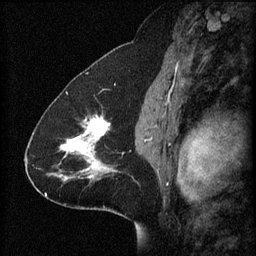
Breast MRI (dynamic contrast-enhanced), one sagittal slice; position 39 of 60 along the scan axis; 3 images stored at this slice position (order not interpretable as contrast timing); 1.5 T; TE 4.2 ms, TR 8.2 ms; 2 mm slice thickness; 256 × 256 image matrix, field of view 200 × 200 mm. Patient: female, 41 years.
Annotated regions visible in this slice (semi-automatically segmented with operator editing):
- analysis volume of interest (the breast-tissue region the enhancement analysis was run in; not a lesion): box from (x=58, y=114) to (x=120, y=181) px
- tumour enhancement mask (voxels above the 70 % enhancement threshold inside the analysis volume of interest): (x=61, y=116)–(x=113, y=181)